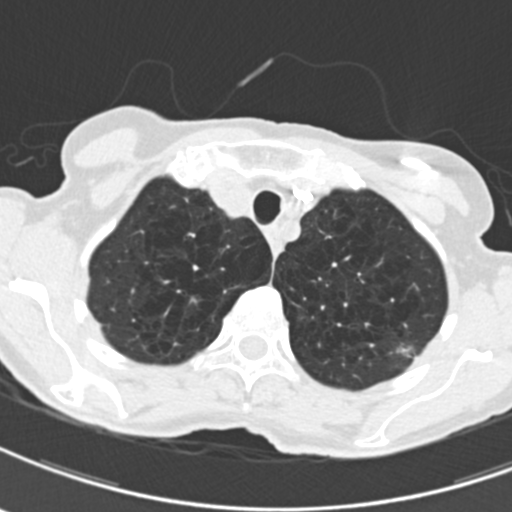
Axial slice from a low-dose chest CT screening exam. Third annual screen. Lung window (W 1500 / L -600 HU). 512 × 512 image matrix, field of view 279 × 279 mm. Female, age 71 years at enrolment. Current smoker at enrolment.
- Lesion marked by an expert reader, bounding box (x1, y1, x2, y2) in pixels: (383, 333, 425, 373).
- Screening reader's record for this exam (one nodule recorded; not confirmed to be the boxed lesion): non-calcified nodule or mass ≥4 mm, left upper lobe, 12 × 9 mm, spiculated (stellate) margins, mixed attenuation, pre-existing on the prior screen: yes; interval growth: yes.
- Official screen result: positive, other.
- Participant outcome: lung cancer diagnosed 114 days after this screen — adenocarcinoma, NOS, left upper lobe, moderately differentiated (G2), stage IA (AJCC 6th edition), 12 mm at pathology.